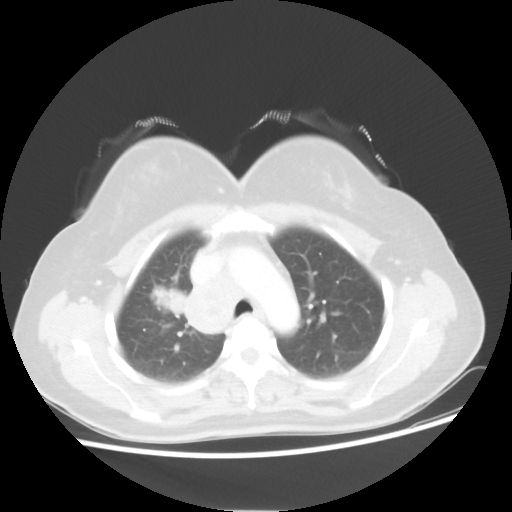
Chest CT, one axial slice; position 37 of 50 along the scan axis; reconstruction kernel STANDARD; 100 kVp; lung window (W 1500 / L -600 HU); 5 mm slice thickness; 512 × 512 image matrix. Female patient, age 40 years. Case-level facts recorded for this patient, not image findings: clinical TNM (as recorded): T1c N3 M0; histopathological grade: G3.
Structures marked on this image (bounding box drawn by a radiologist):
- lung tumour (recorded histology: small cell carcinoma): box from (x=148, y=284) to (x=184, y=321) px